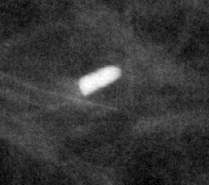
Region of interest cut from a scanned film mammogram (one marked finding), right breast, CC view, BI-RADS breast density category 1 (scale 1–4).
Calcifications, morphology large rodlike, distribution segmental; BI-RADS assessment category 2; subtlety rating 5 on a 1 (subtle) to 5 (obvious) scale; benign; no additional work-up was recommended (benign without callback).